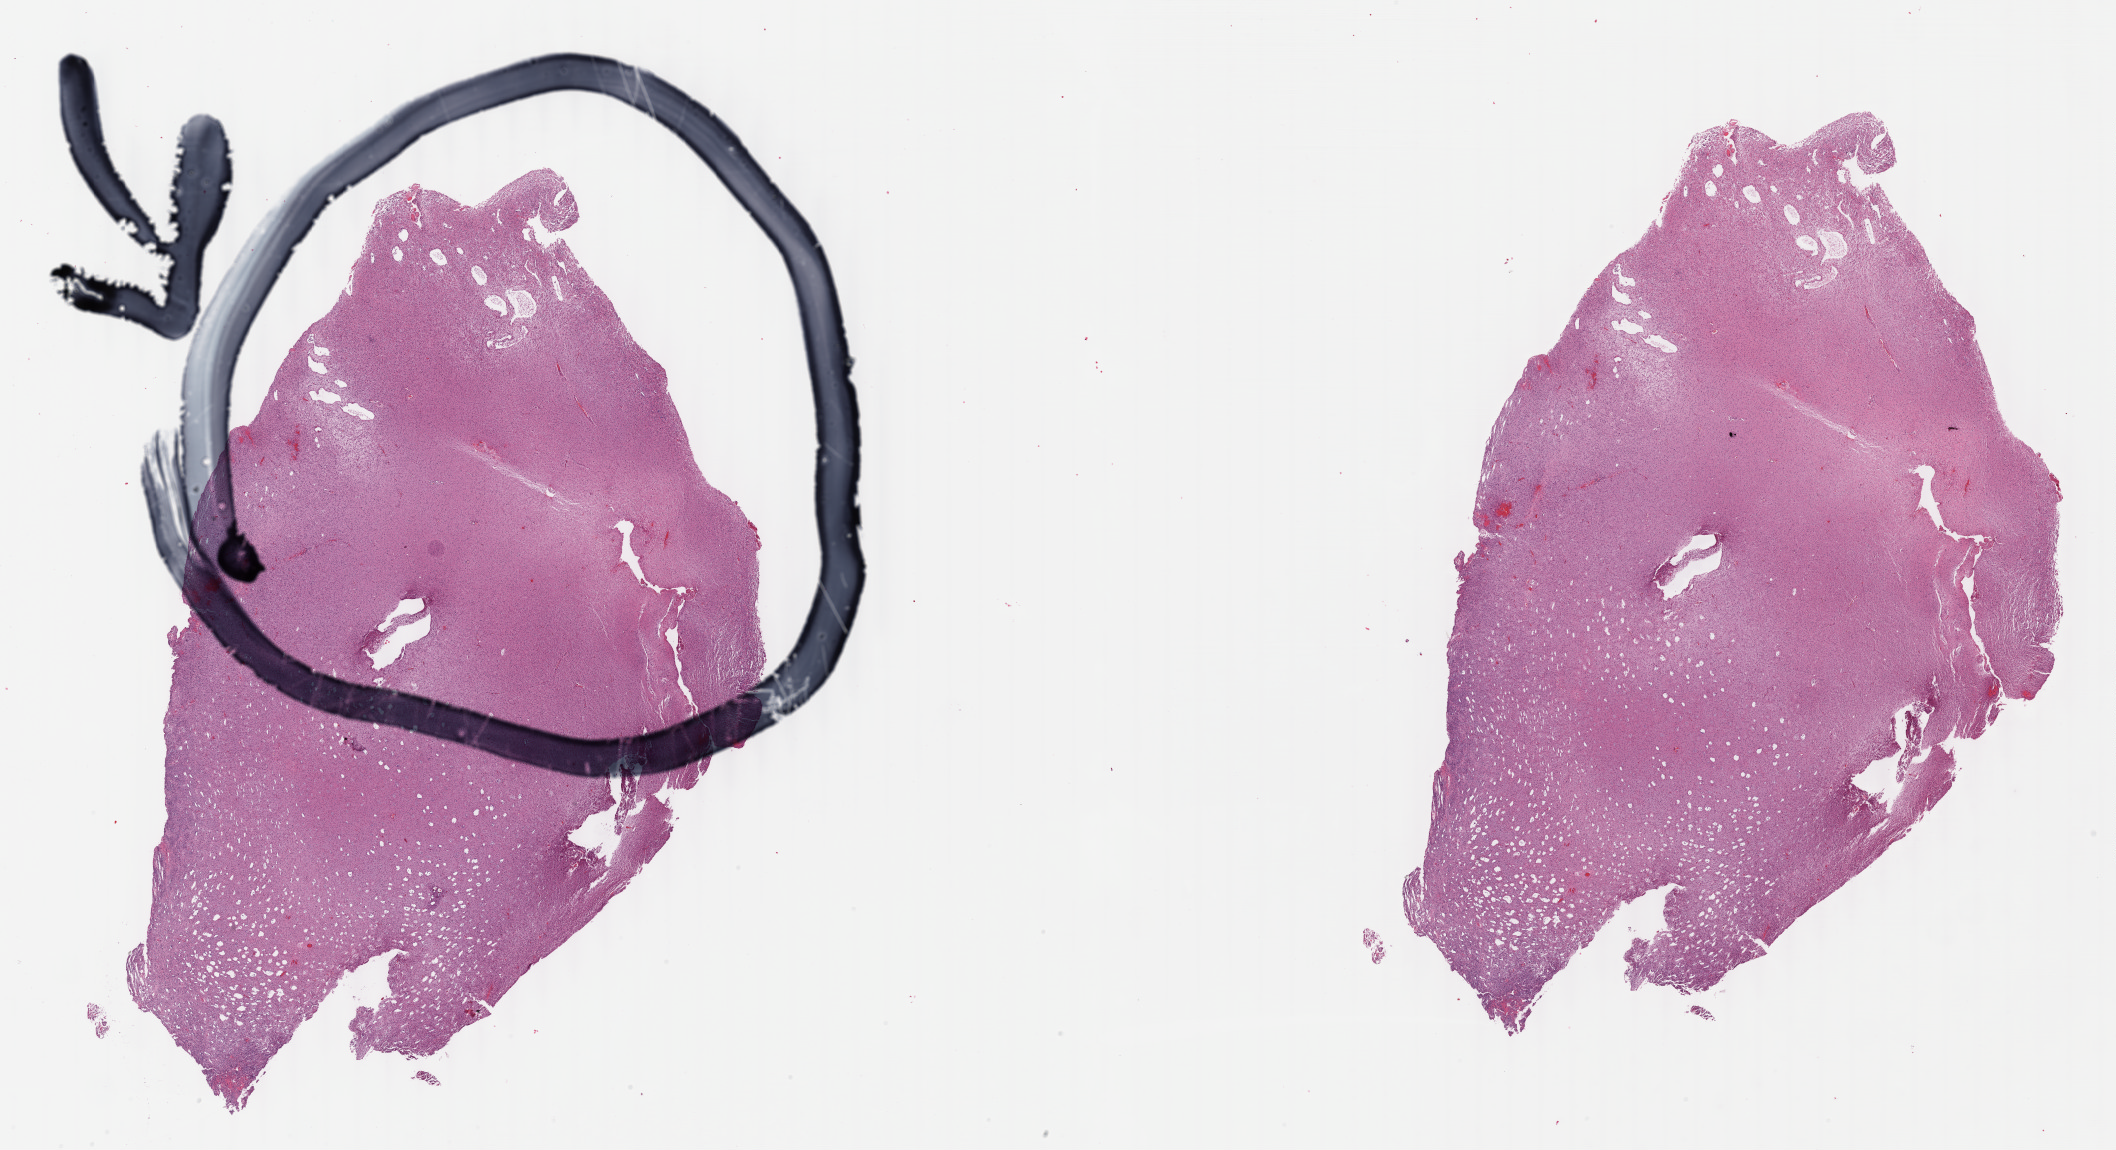
Whole-slide histology image, Hematoxylin and eosin (H&E) stained — a low-resolution overview of the entire scanned area, about 34.2 x 18.6 mm (slide scanned at 40x); formalin-fixed paraffin-embedded (FFPE) diagnostic section; primary tumour sample from the brain. Male patient; age at initial diagnosis 36 years. Histologic grade: G2 (moderately differentiated).
• diagnosis: Mixed glioma (cerebrum)
• laterality: right